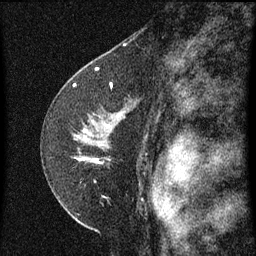
Breast MRI (dynamic contrast-enhanced), one sagittal slice; dynamic contrast-enhanced series, image 2 of 3 at this slice position (ordered by acquisition); 1.5 T; TE 4.2 ms, TR 8 ms; 2 mm slice thickness; 256 × 256 image matrix. Patient: female, 47 years.
Annotated regions visible in this slice (semi-automatic segmentation, software-assisted and operator-edited):
- analysis volume of interest (the breast-tissue region the enhancement analysis was run in; not a lesion): bounding box [x1, y1, x2, y2] px = [50, 84, 141, 199]
- tumour enhancement mask (voxels above the 70 % enhancement threshold inside the analysis volume of interest): [74, 86, 101, 165]